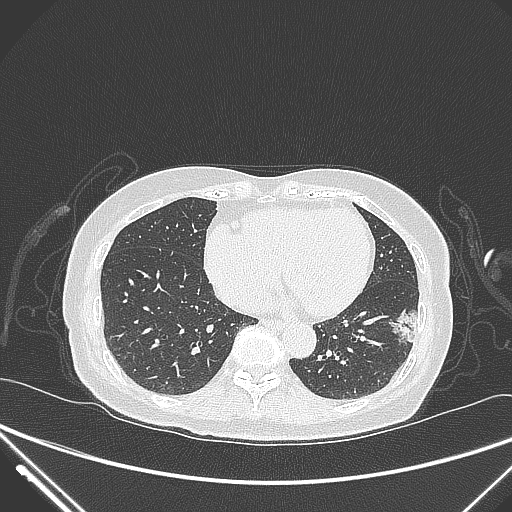
Chest CT, one axial slice. Position 107 of 310 along the scan axis. 120 kVp. Lung window (W 1500 / L -600 HU). 512 × 512 image matrix. Patient: female, 82 years. Case-level facts recorded for this patient, not image findings: clinical TNM (as recorded): T1c N0 M0; histopathological grade: G2.
Annotated regions visible in this slice (bounding box drawn by a radiologist):
- lung tumour (recorded histology: adenocarcinoma): bounding box (x1, y1, x2, y2) in pixels: (386, 306, 437, 352)